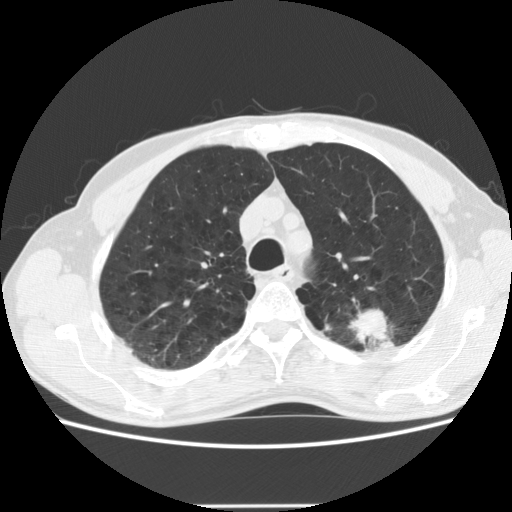
Low-dose screening chest CT, one axial slice; slice 149 of 191 in the series (ordered by position); reconstruction kernel STANDARD; 120 kVp; lung window (W 1500 / L -600 HU); 2.5 mm slice thickness; 512 × 512 image matrix, field of view 352 × 352 mm.
Annotated regions visible in this slice (outlined manually by an expert reader):
- lesion 1 (tumor, upper lobe of left lung): bounding box [x1, y1, x2, y2] px = [351, 309, 390, 344]